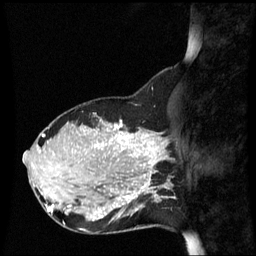
Breast MRI (dynamic contrast-enhanced), one sagittal slice; slice 21 of 60 in the series (ordered by position); dynamic contrast-enhanced series, image 2 of 3 at this slice position (ordered by acquisition); 1.5 T; TE 4.2 ms, TR 8.9 ms; 256 × 256 image matrix. Patient: female, 31 years. Case-level facts recorded for this patient, not image findings: setting: breast cancer imaged before/during neoadjuvant chemotherapy; receptor status: HR-positive, HER2-negative.
Annotated regions visible in this slice (semi-automatically segmented with operator editing):
- analysis volume of interest (the breast-tissue region the enhancement analysis was run in; not a lesion): bounding box (x1, y1, x2, y2) in pixels: (90, 180, 152, 235)
- tumour enhancement mask (voxels above the 70 % enhancement threshold inside the analysis volume of interest): (128, 182, 152, 199)